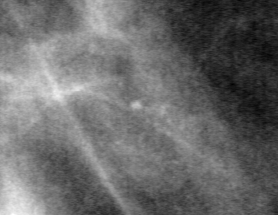
Cropped region of a digitized screen-film mammogram centred on a radiologist-marked abnormality, right breast, MLO view.
- Finding: calcifications, morphology pleomorphic, distribution clustered; BI-RADS assessment category 4; pathology result (as recorded, not read from the image): benign.